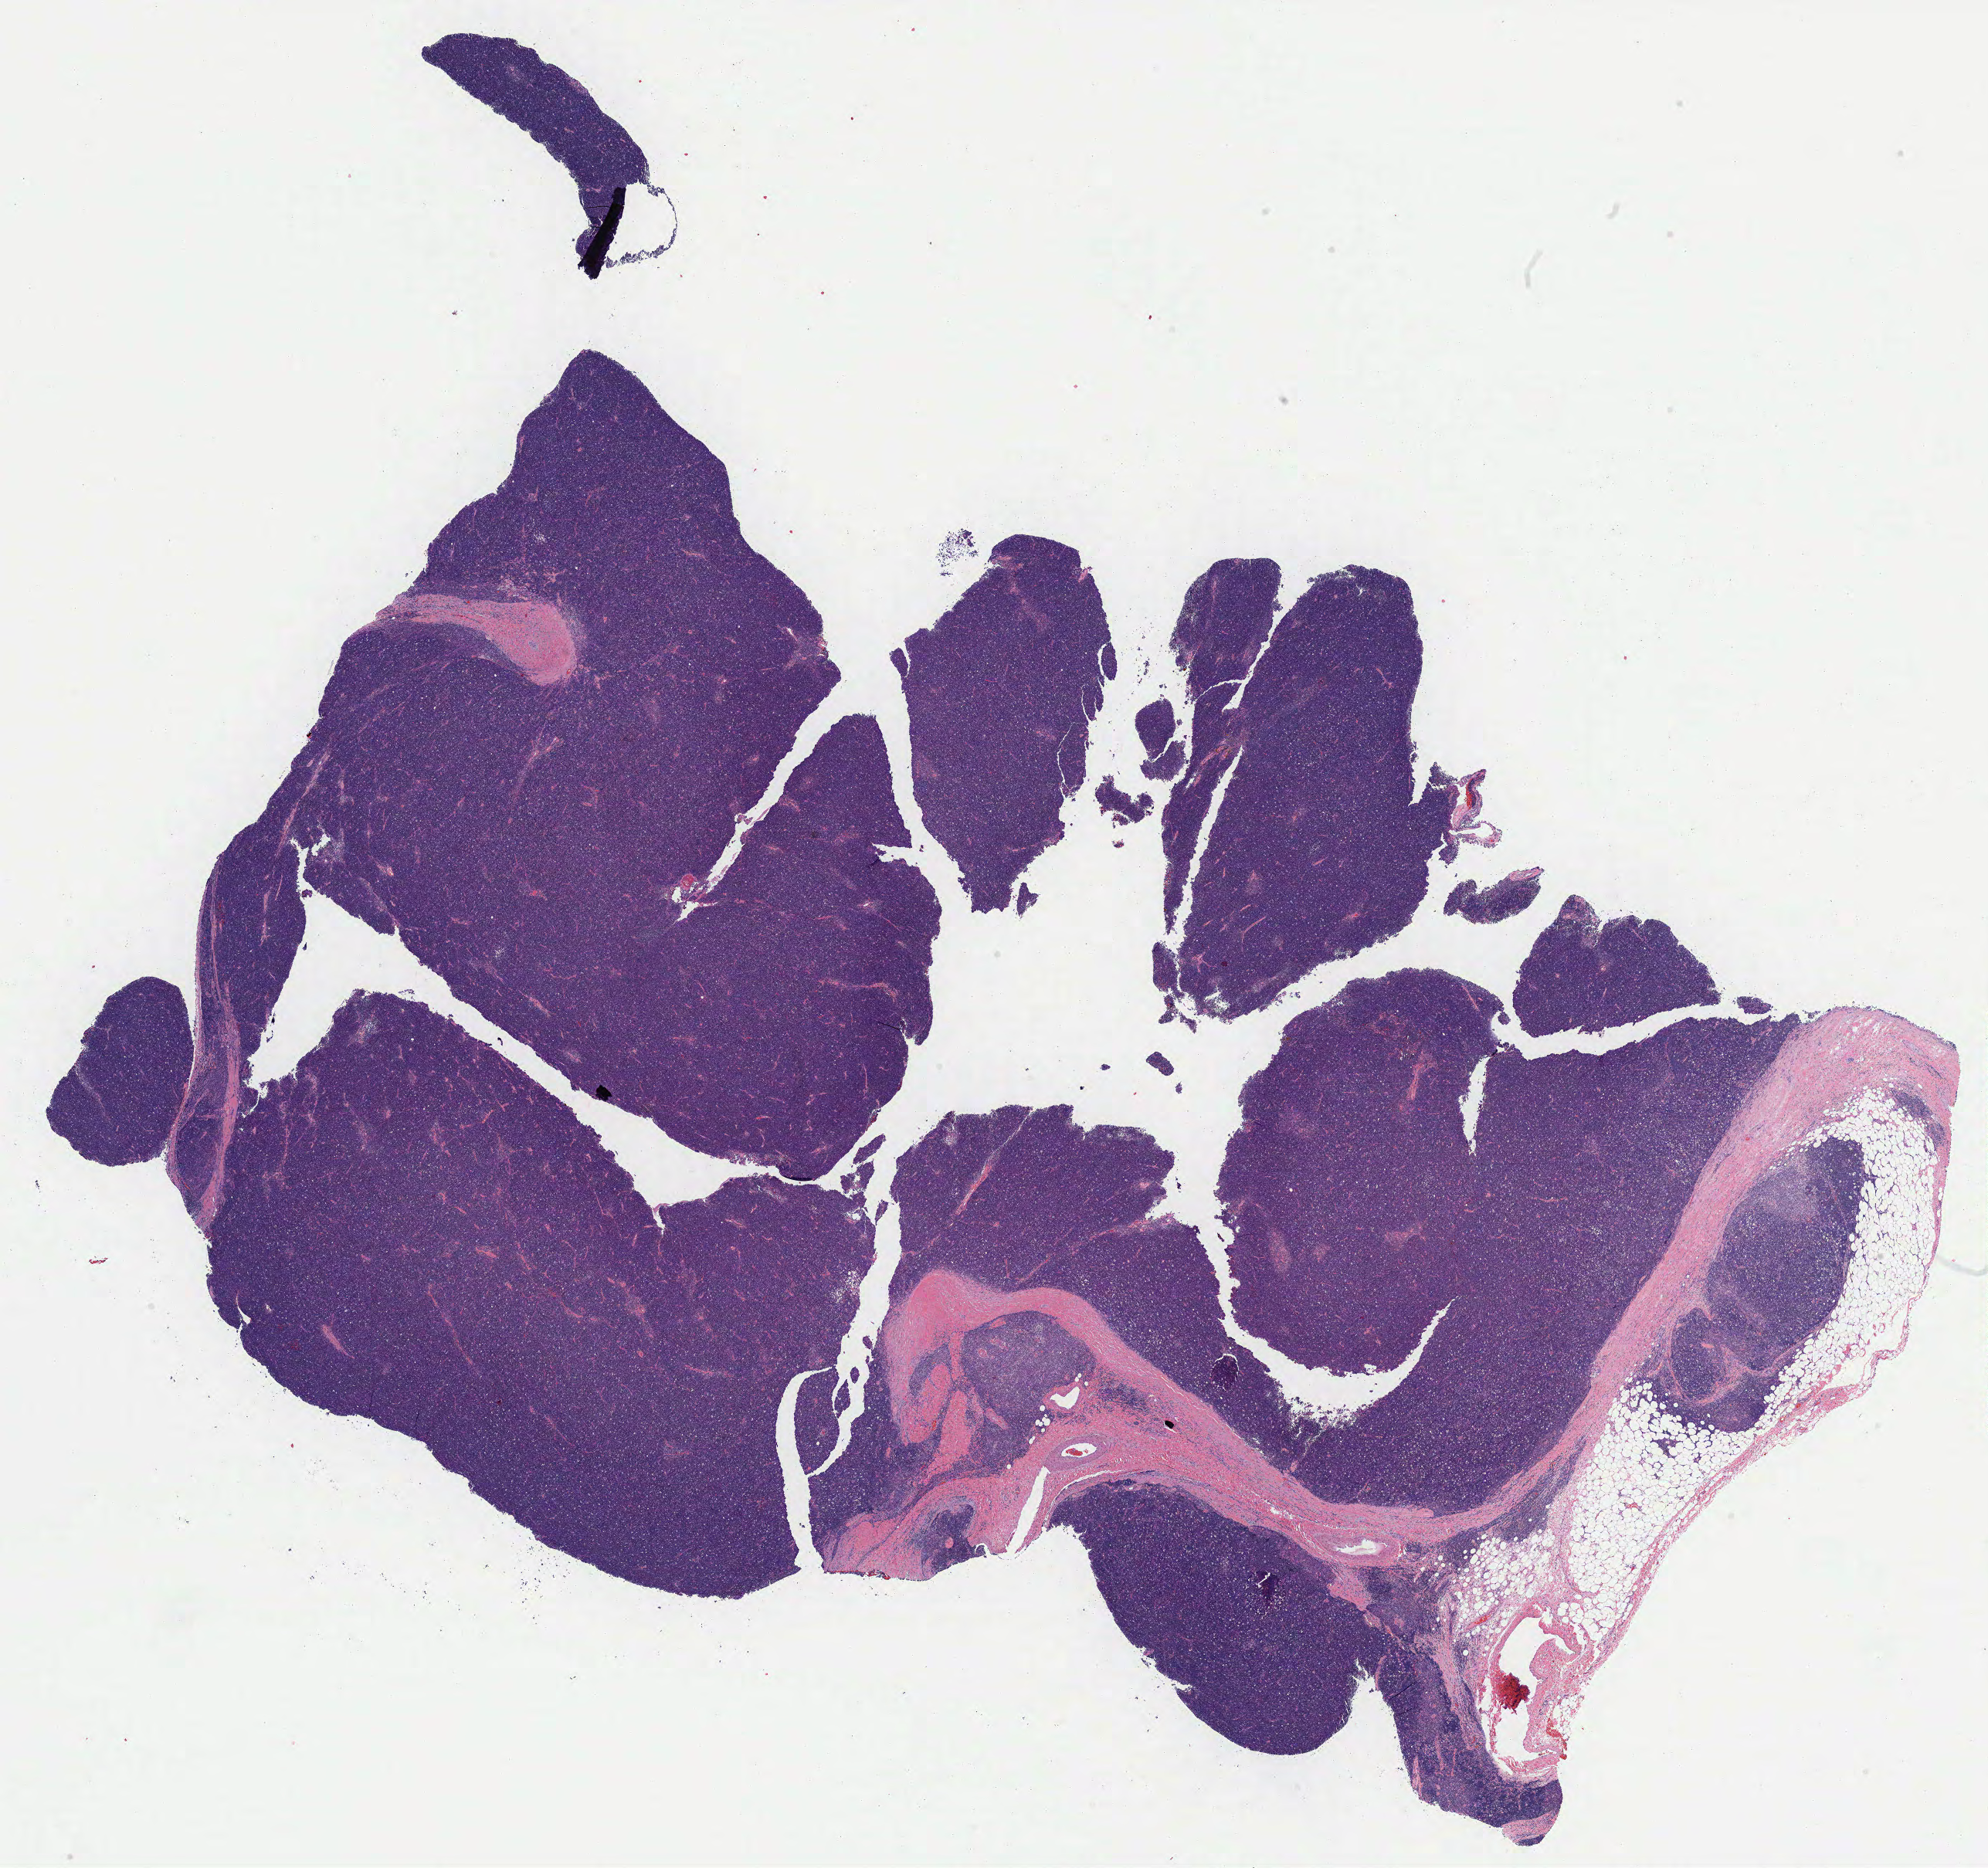
Digitized Hematoxylin and eosin (H&E) stained tissue section (whole slide) — low-resolution overview of the scanned area, about 21.0 x 19.7 mm (slide scanned at 40x), formalin-fixed paraffin-embedded (FFPE) diagnostic section, thymus, primary tumour sample. Patient: female, age at initial diagnosis 55 years.
Diagnosis: Thymoma, type B1, NOS.